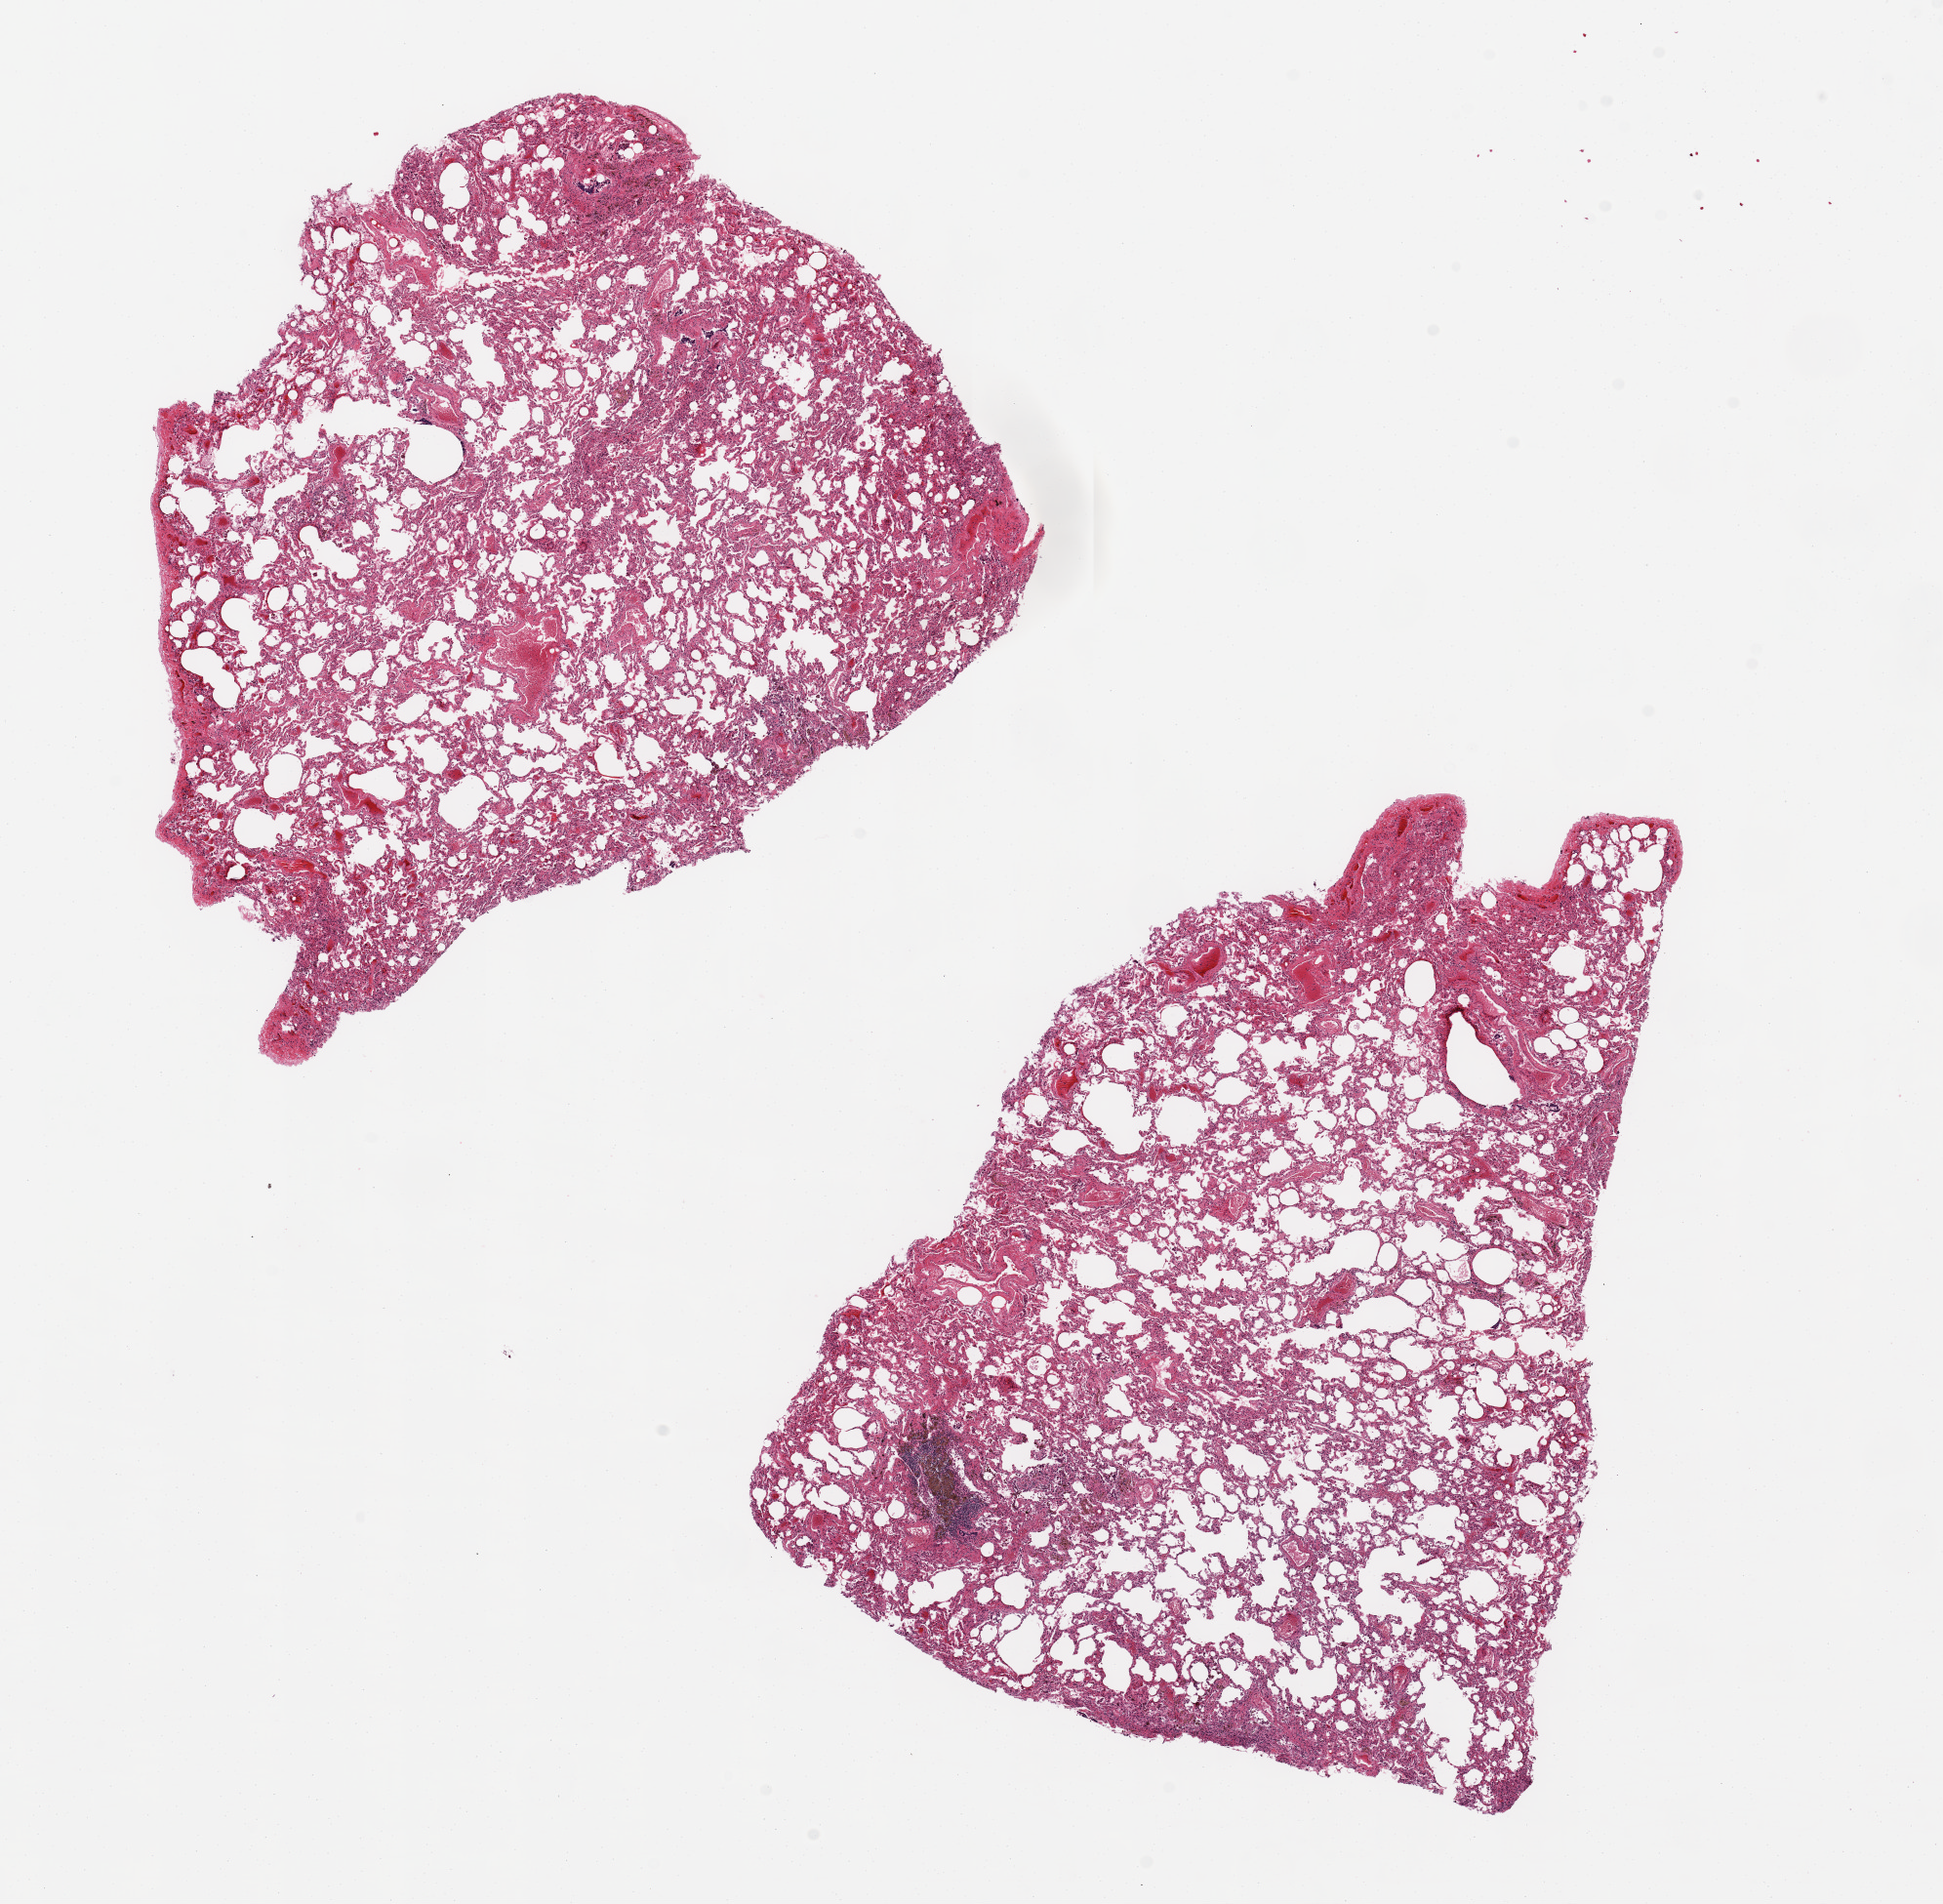
Digitized H&E-stained section, brightfield, a low-resolution overview of the entire scanned area, about 15.8 x 15.4 mm, PAXgene-fixed paraffin-embedded (PFPE) section, target tissue: lung, donor tissue sample. Donor: female.
Reviewer comment on this tissue sample: 2 ~7x6mm aliquots, evidence of chronic pulmonary congestion (aggregates of hemosiderin-laden macrophages).